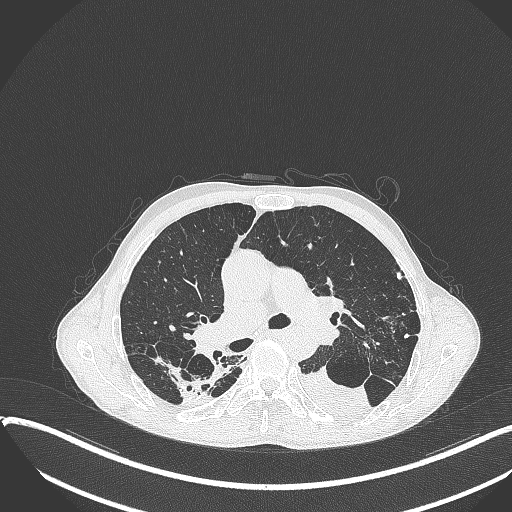
Chest CT, one axial slice; position 238 of 401 along the scan axis; 120 kVp; lung window (W 1500 / L -600 HU); 1 mm slice thickness; 512 × 512 image matrix, field of view 400 × 400 mm. Patient: male, 57 years. From the clinical record (not read from this slice): clinical TNM (as recorded): T4 N0 M0.
Outlined on this slice (bounding box drawn by a radiologist):
- lung tumour (recorded histology: squamous cell carcinoma): box from (x=298, y=361) to (x=375, y=420) px